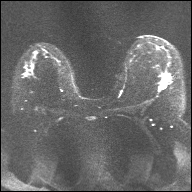
Breast MRI, one axial slice. Position 19 of 32 along the scan axis. Diffusion-weighted series; image 2 of 4 stored at this slice position (different b-values; order by instance number). 1.5 T. 4 mm slice thickness. 192 × 192 image matrix, field of view 360 × 360 mm. Female patient.
Structures marked on this image (expert manual segmentation):
- tumour on diffusion-weighted imaging: bounding box (x1, y1, x2, y2) in pixels: (161, 75, 169, 89)